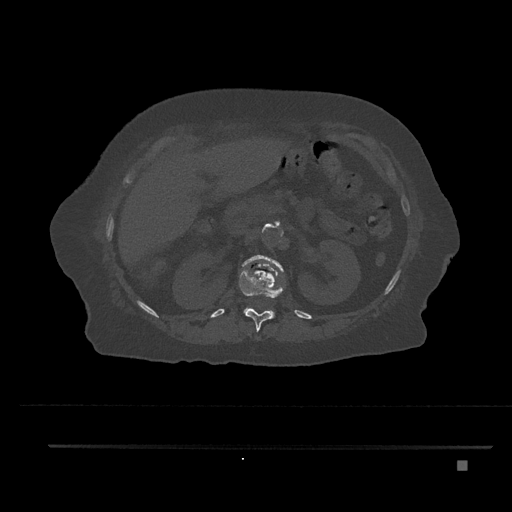
CT including the spine, one axial slice; slice 249 of 797 in the series (ordered by position); 120 kVp; bone window (W 1800 / L 400 HU); 512 × 512 image matrix, field of view 437 × 437 mm. Patient: female, 76 years. Case-level facts recorded for this patient, not image findings: primary cancer: lung; vertebrae with lytic lesions (as recorded): T11, L3.
Structures marked on this image (semi-automatic segmentation, software-assisted and operator-edited):
- L1 vertebra: box from (x=242, y=255) to (x=285, y=316) px
- T12 vertebra: (x=239, y=270)–(x=284, y=332)